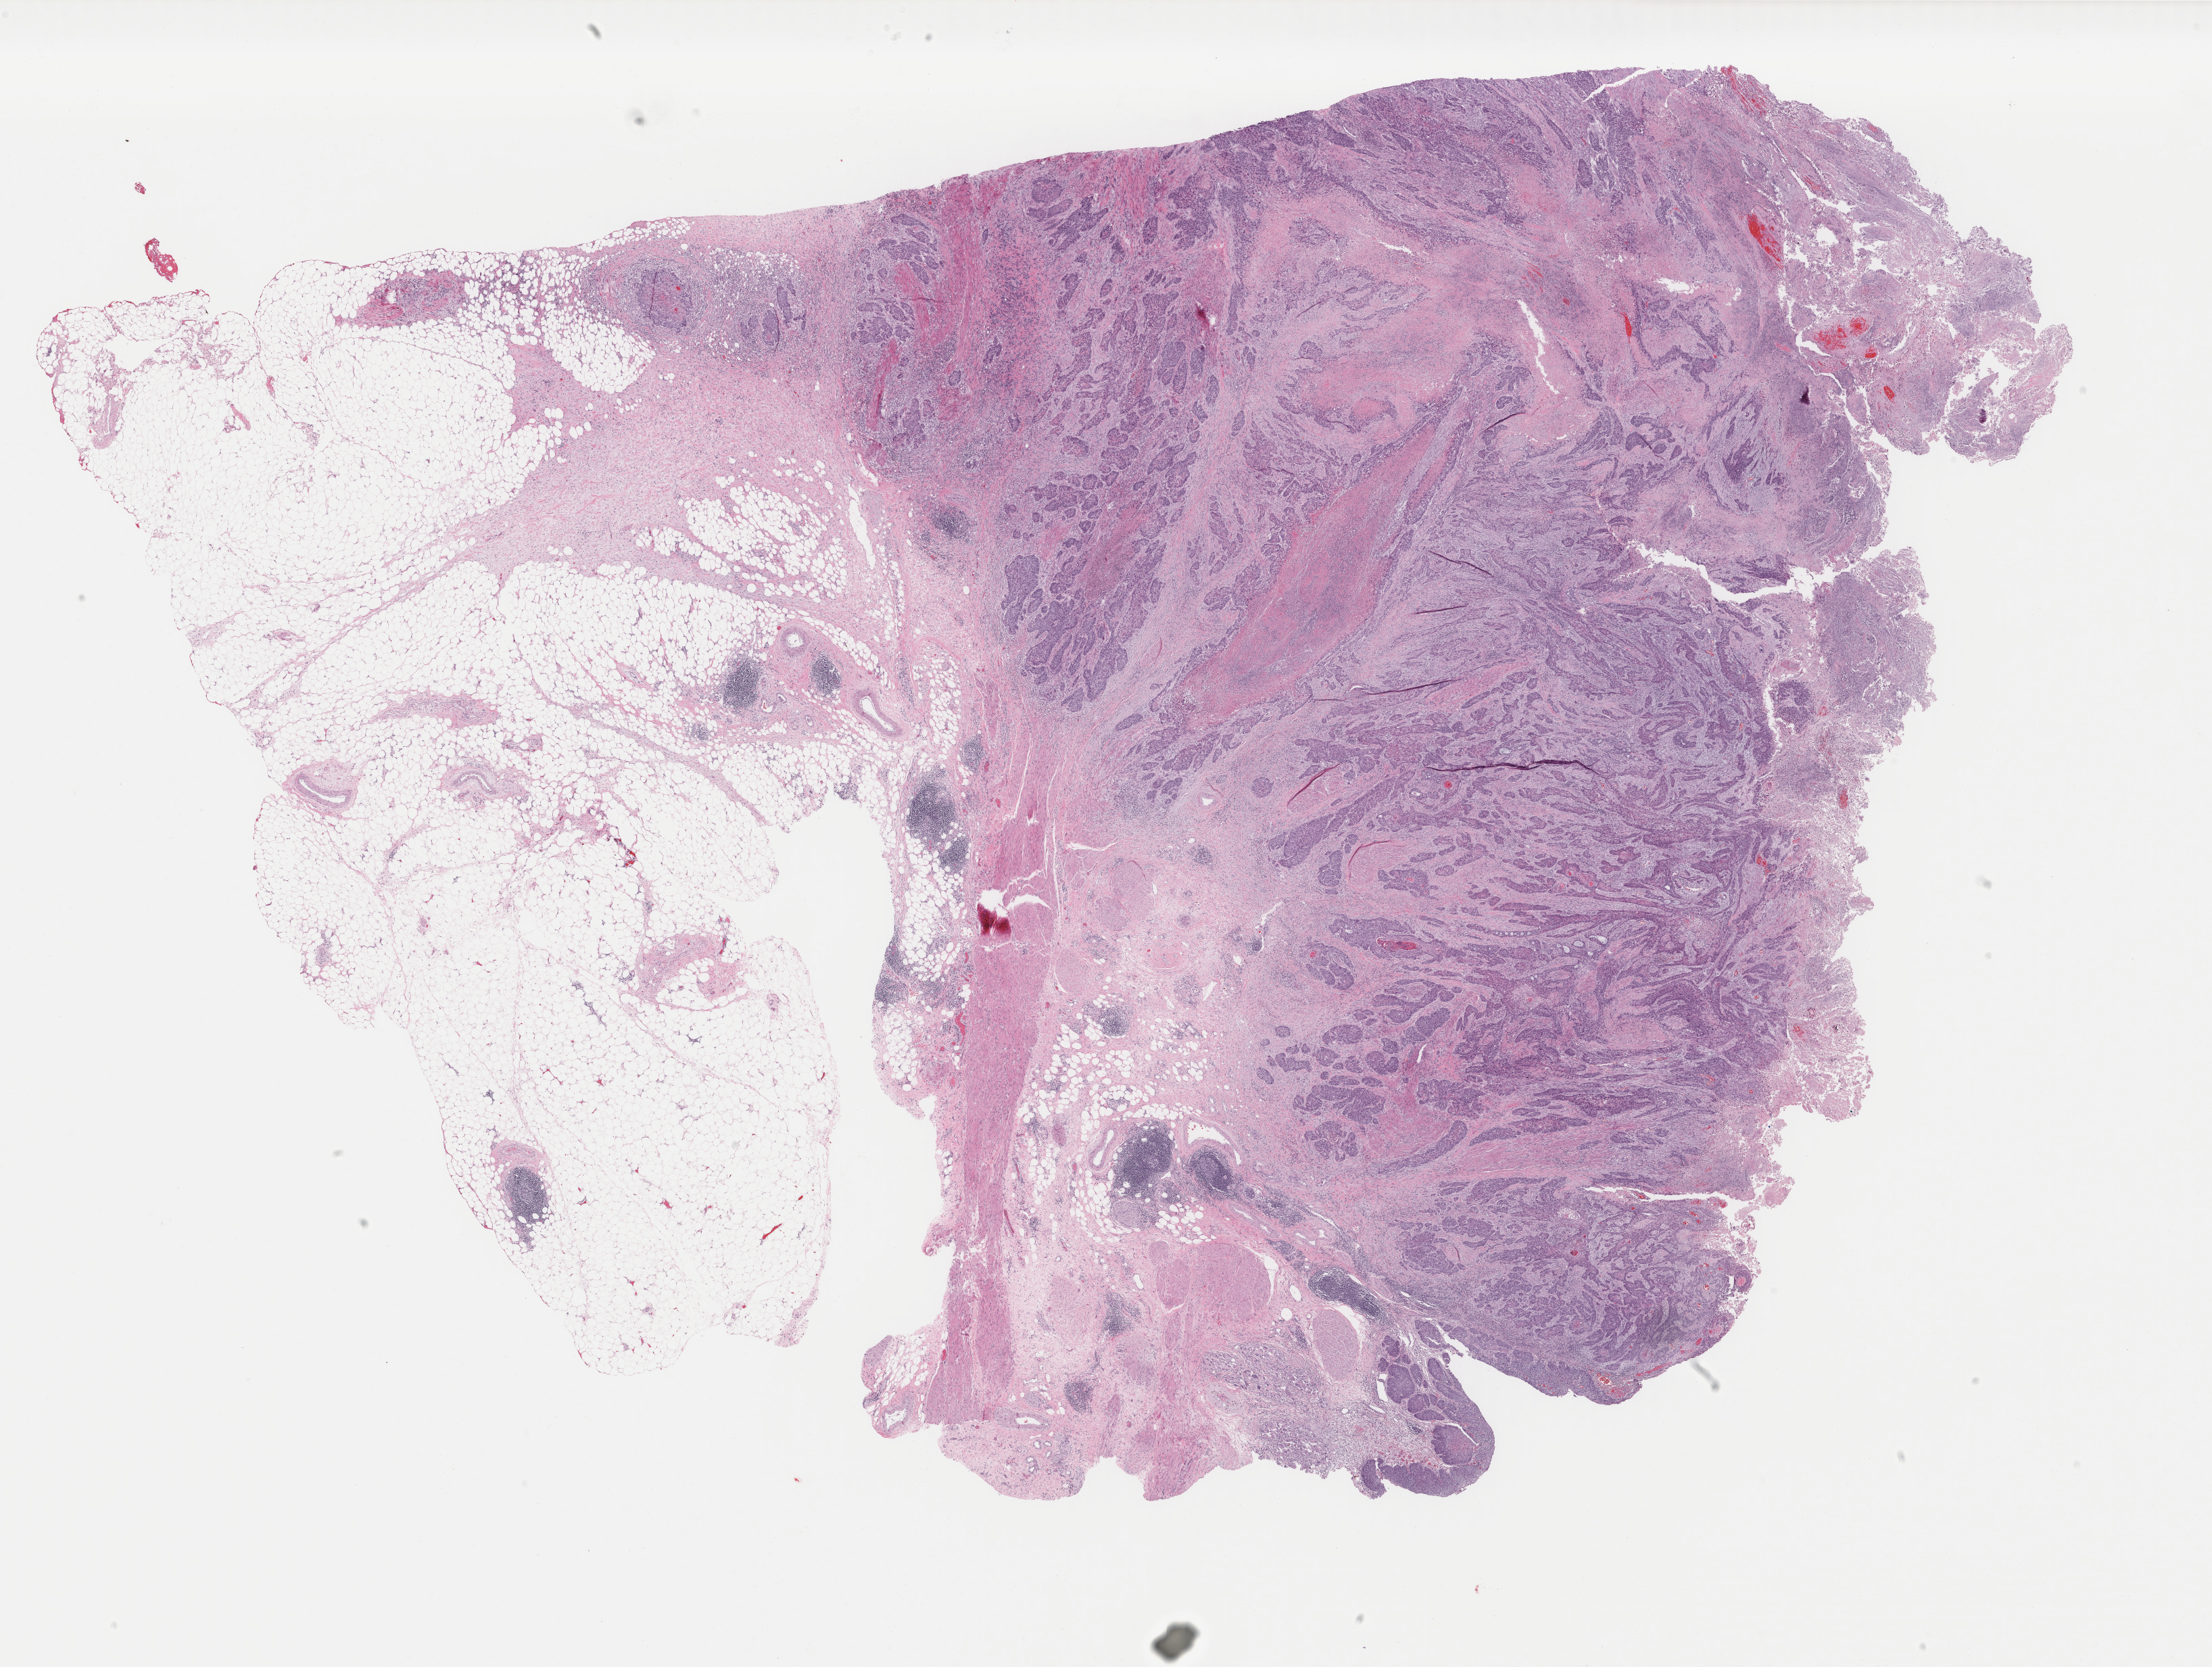
H&E-stained whole-slide image, low-resolution overview of the scanned area, about 26.0 x 19.6 mm (slide scanned at 40x). Formalin-fixed paraffin-embedded (FFPE) diagnostic section. Sample: primary tumour, bladder. Male patient; age at initial diagnosis 67 years.
Pathologic diagnosis: Transitional cell carcinoma.